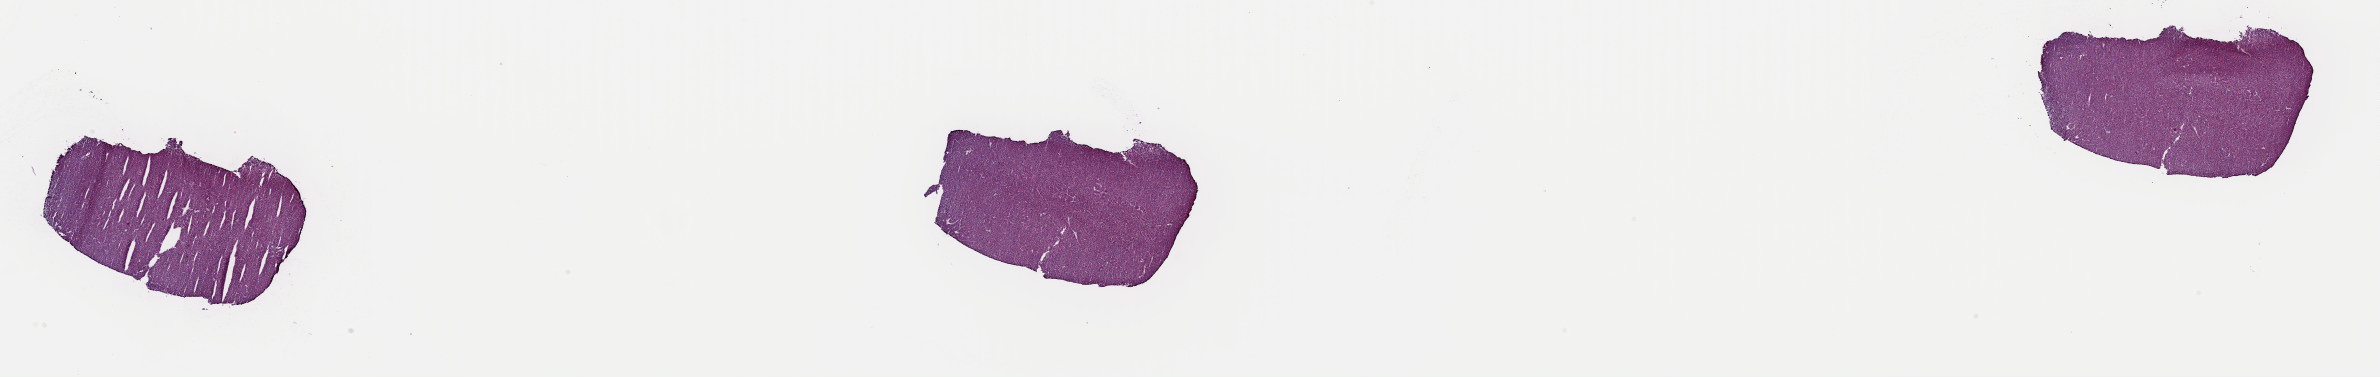
H&E whole-slide image, low-resolution overview of the scanned area, about 37.6 x 6.0 mm, frozen section from the top of the tissue portion, liver, primary tumour sample. Female, age 68 years at initial diagnosis. Histologic grade: G1 (well differentiated). Pathologist review of this section (percent, as recorded): tumour cells 98%, tumour nuclei 97%, normal cells 0%, stromal cells 2%, necrosis 0%. Infiltration values recorded for this section: lymphocyte infiltration 1%, monocyte infiltration 0%, neutrophil infiltration 0%.
AJCC pathologic stage: II. Diagnosis: Hepatocellular carcinoma, NOS.